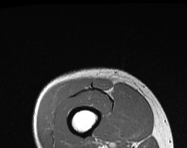
MRI of an extremity soft-tissue mass, one axial slice. Slice 27 of 114 in the series (ordered by position). MR volume resampled by the dataset authors to the PET/CT grid (not the native acquisition matrix). 3.27 mm slice thickness. 187 × 148 image matrix, field of view 183 × 145 mm. Male patient. Case-level facts recorded for this patient, not image findings: histological type: pleiomorphic leiomyosarcoma; grade: intermediate; site of the primary tumour: right thigh.
Structures marked on this image (expert contour drawn on MRI and transferred to this co-registered scan by the dataset authors):
- gross tumour volume including surrounding oedema: bounding box (x1, y1, x2, y2) in pixels: (95, 79, 110, 89)